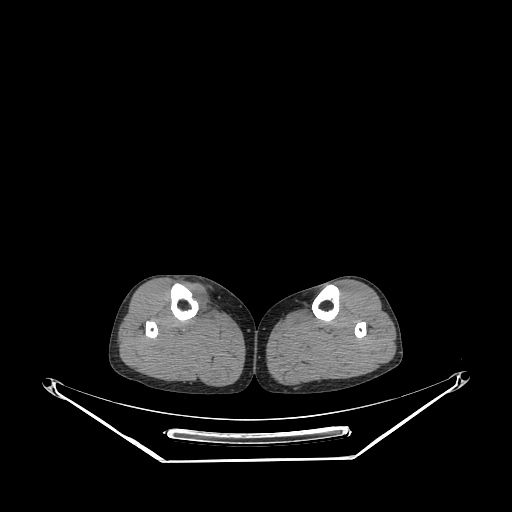
CT of an extremity soft-tissue mass (from a PET/CT study), one axial slice; position 138 of 267 along the scan axis; reconstruction kernel STANDARD; 140 kVp; soft-tissue window (W 400 / L 40 HU); 3.75 mm slice thickness; 512 × 512 image matrix, field of view 500 × 500 mm. Female patient. From the clinical record (not read from this slice): histological type: undifferentiated – high grade; grade: high; site of the primary tumour: right thigh.
Structures marked on this image (expert contour drawn on MRI and transferred to this co-registered scan by the dataset authors):
- gross tumour volume (mass): box from (x=187, y=285) to (x=209, y=314) px